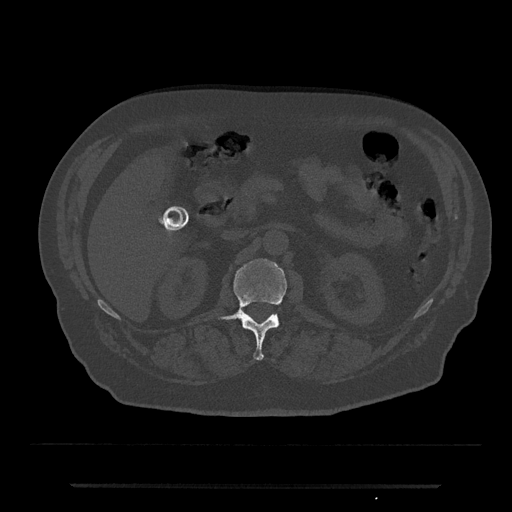
CT including the spine, one axial slice; slice 528 of 797 in the series (ordered by position); 120 kVp; bone window (W 1800 / L 400 HU); 0.5 mm slice thickness; 512 × 512 image matrix, field of view 434 × 434 mm. Patient: male, 80 years. From the clinical record (not read from this slice): primary cancer: prostate; vertebrae with lytic lesions (as recorded): L1, T11.
Annotated regions visible in this slice (semi-automatic segmentation, software-assisted and operator-edited):
- L1 vertebra: bounding box [x1, y1, x2, y2] px = [223, 259, 288, 360]